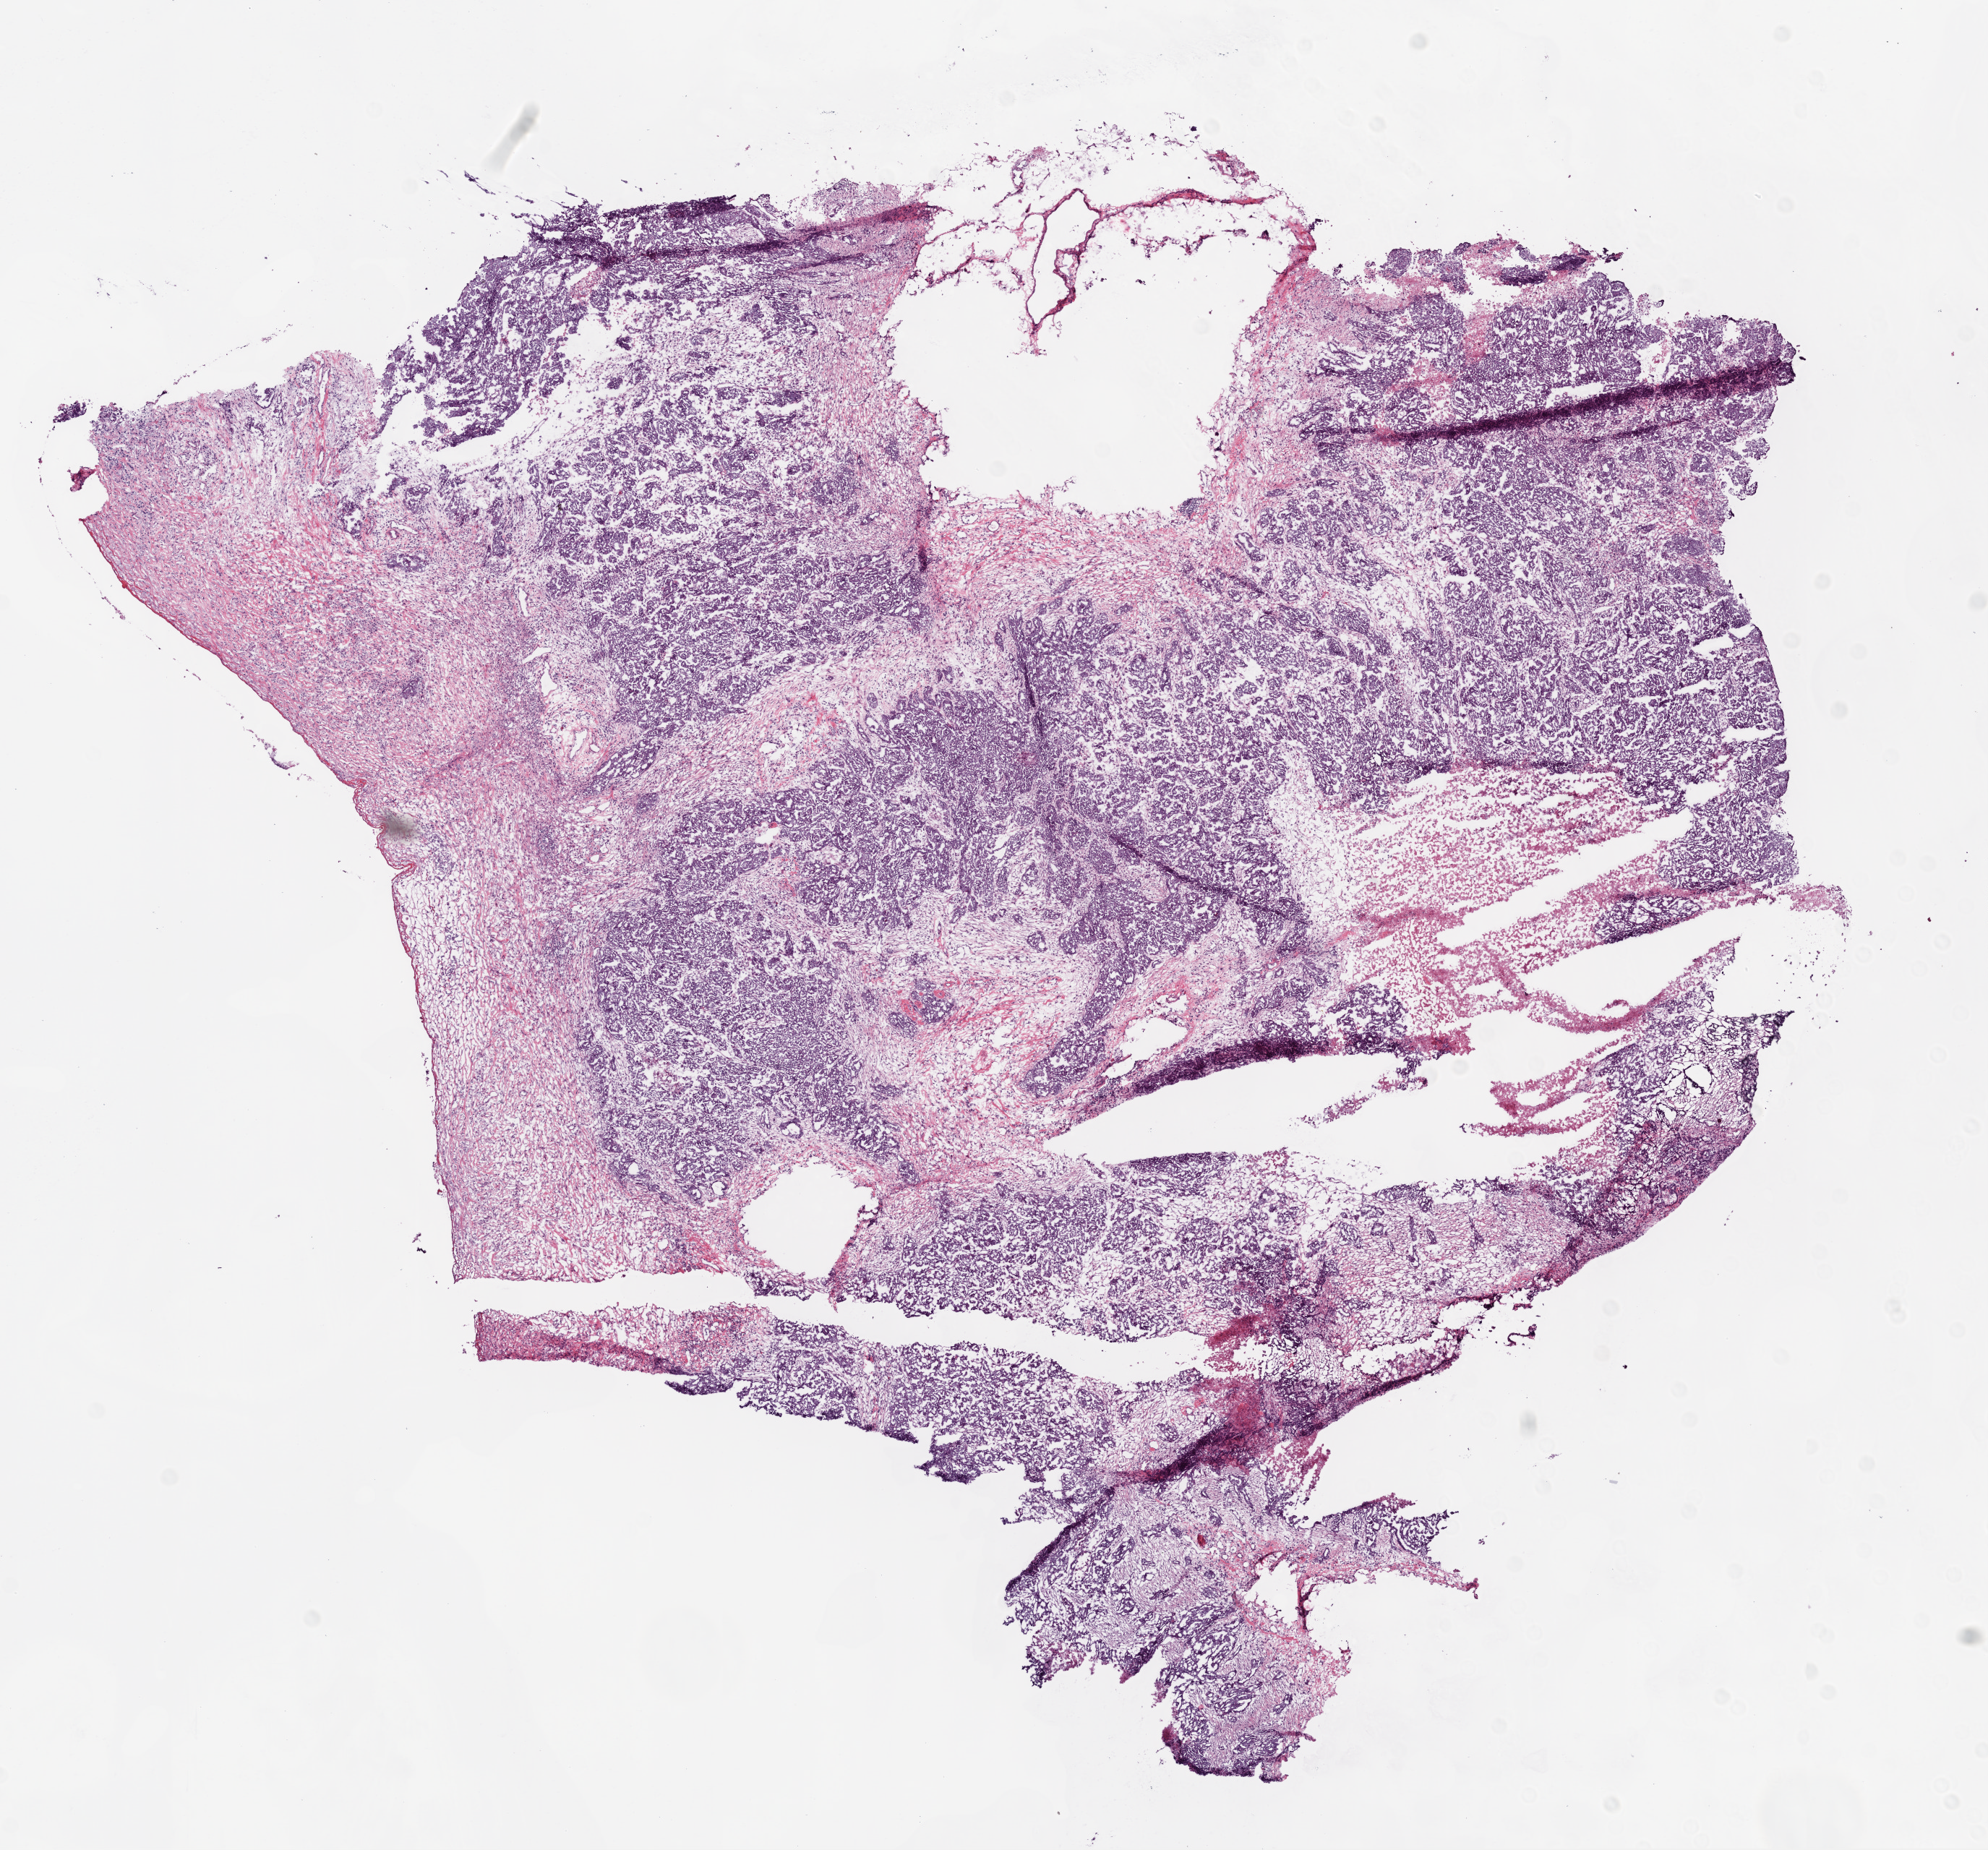
Whole-slide histology image, Hematoxylin and eosin (H&E) stained, a low-resolution overview of the entire scanned area, about 11.0 x 10.3 mm (from a 20x scan). Frozen section. Primary tumour sample from the ovary. Female patient; age at initial diagnosis 65 years. Histologic grade: G2 (moderately differentiated). Composition of this section per pathologist review: tumour cells 60%, tumour nuclei 70%, normal cells 0%, stromal cells 40%, necrosis 0%.
• diagnosis: Serous cystadenocarcinoma, NOS
• FIGO stage: IV